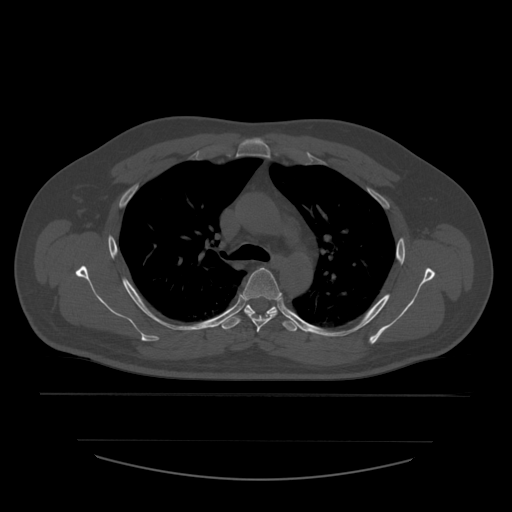
CT including the spine, one axial slice; slice 410 of 532 in the series (ordered by position); reconstruction kernel STANDARD; 120 kVp; bone window (W 1800 / L 400 HU); 1.25 mm slice thickness; 512 × 512 image matrix, field of view 441 × 441 mm. Patient age 44 years. From the clinical record (not read from this slice): primary cancer: soft tissue sarcoma.
Annotated regions visible in this slice (semi-automatic segmentation, software-assisted and operator-edited):
- T4 vertebra: box from (x=242, y=268) to (x=282, y=333) px
- T5 vertebra: (x=220, y=305)–(x=298, y=332)